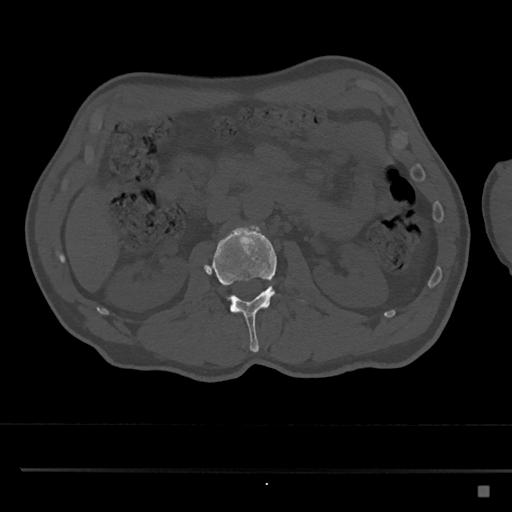
CT including the spine, one axial slice; slice 752 of 797 in the series (ordered by position); bone window (W 1800 / L 400 HU); 0.5 mm slice thickness; 512 × 512 image matrix, field of view 391 × 391 mm. Patient: male, 59 years. From the clinical record (not read from this slice): primary cancer: prostate.
Outlined on this slice (semi-automatically segmented with operator editing):
- L2 vertebra: bounding box (x1, y1, x2, y2) in pixels: (204, 226, 277, 352)